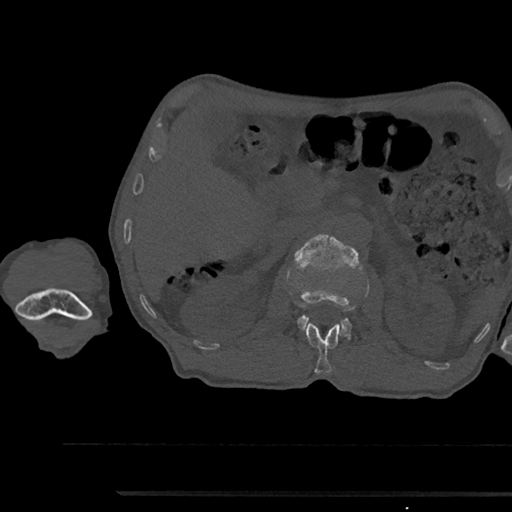
CT including the spine, one axial slice; position 607 of 797 along the scan axis; reconstruction kernel Br40s/3; 120 kVp; bone window (W 1800 / L 400 HU); 512 × 512 image matrix, field of view 367 × 367 mm. Patient: male, 79 years. From the clinical record (not read from this slice): primary cancer: prostate.
Outlined on this slice (semi-automatic segmentation, software-assisted and operator-edited):
- L1 vertebra: bounding box <306,323,340,374> (left, top, right, bottom; pixels)
- L2 vertebra: <294,234,361,339>